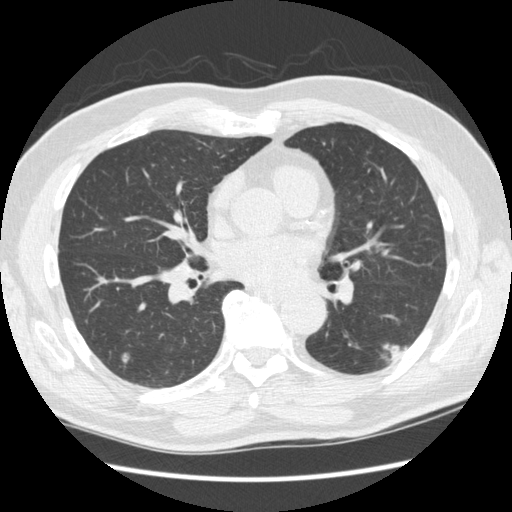
Axial slice from a low-dose chest CT screening exam; baseline screening round; lung window (W 1500 / L -600 HU); 1.25 mm slice thickness. Male, age 74 years at enrolment.
Expert reader's lesion annotation, bounding box <376,324,418,374> (left, top, right, bottom; pixels). The screening reader recorded 3 non-calcified nodules or masses ≥4 mm on this exam (right upper lobe, right lower lobe, left upper lobe); which of them this box marks is not recorded. Later outcome: lung cancer diagnosed 384 days after this screen (after the second annual screen) — squamous cell carcinoma, NOS, left lower lobe, well differentiated (G1), stage IA (AJCC 6th edition), 28 mm at pathology.